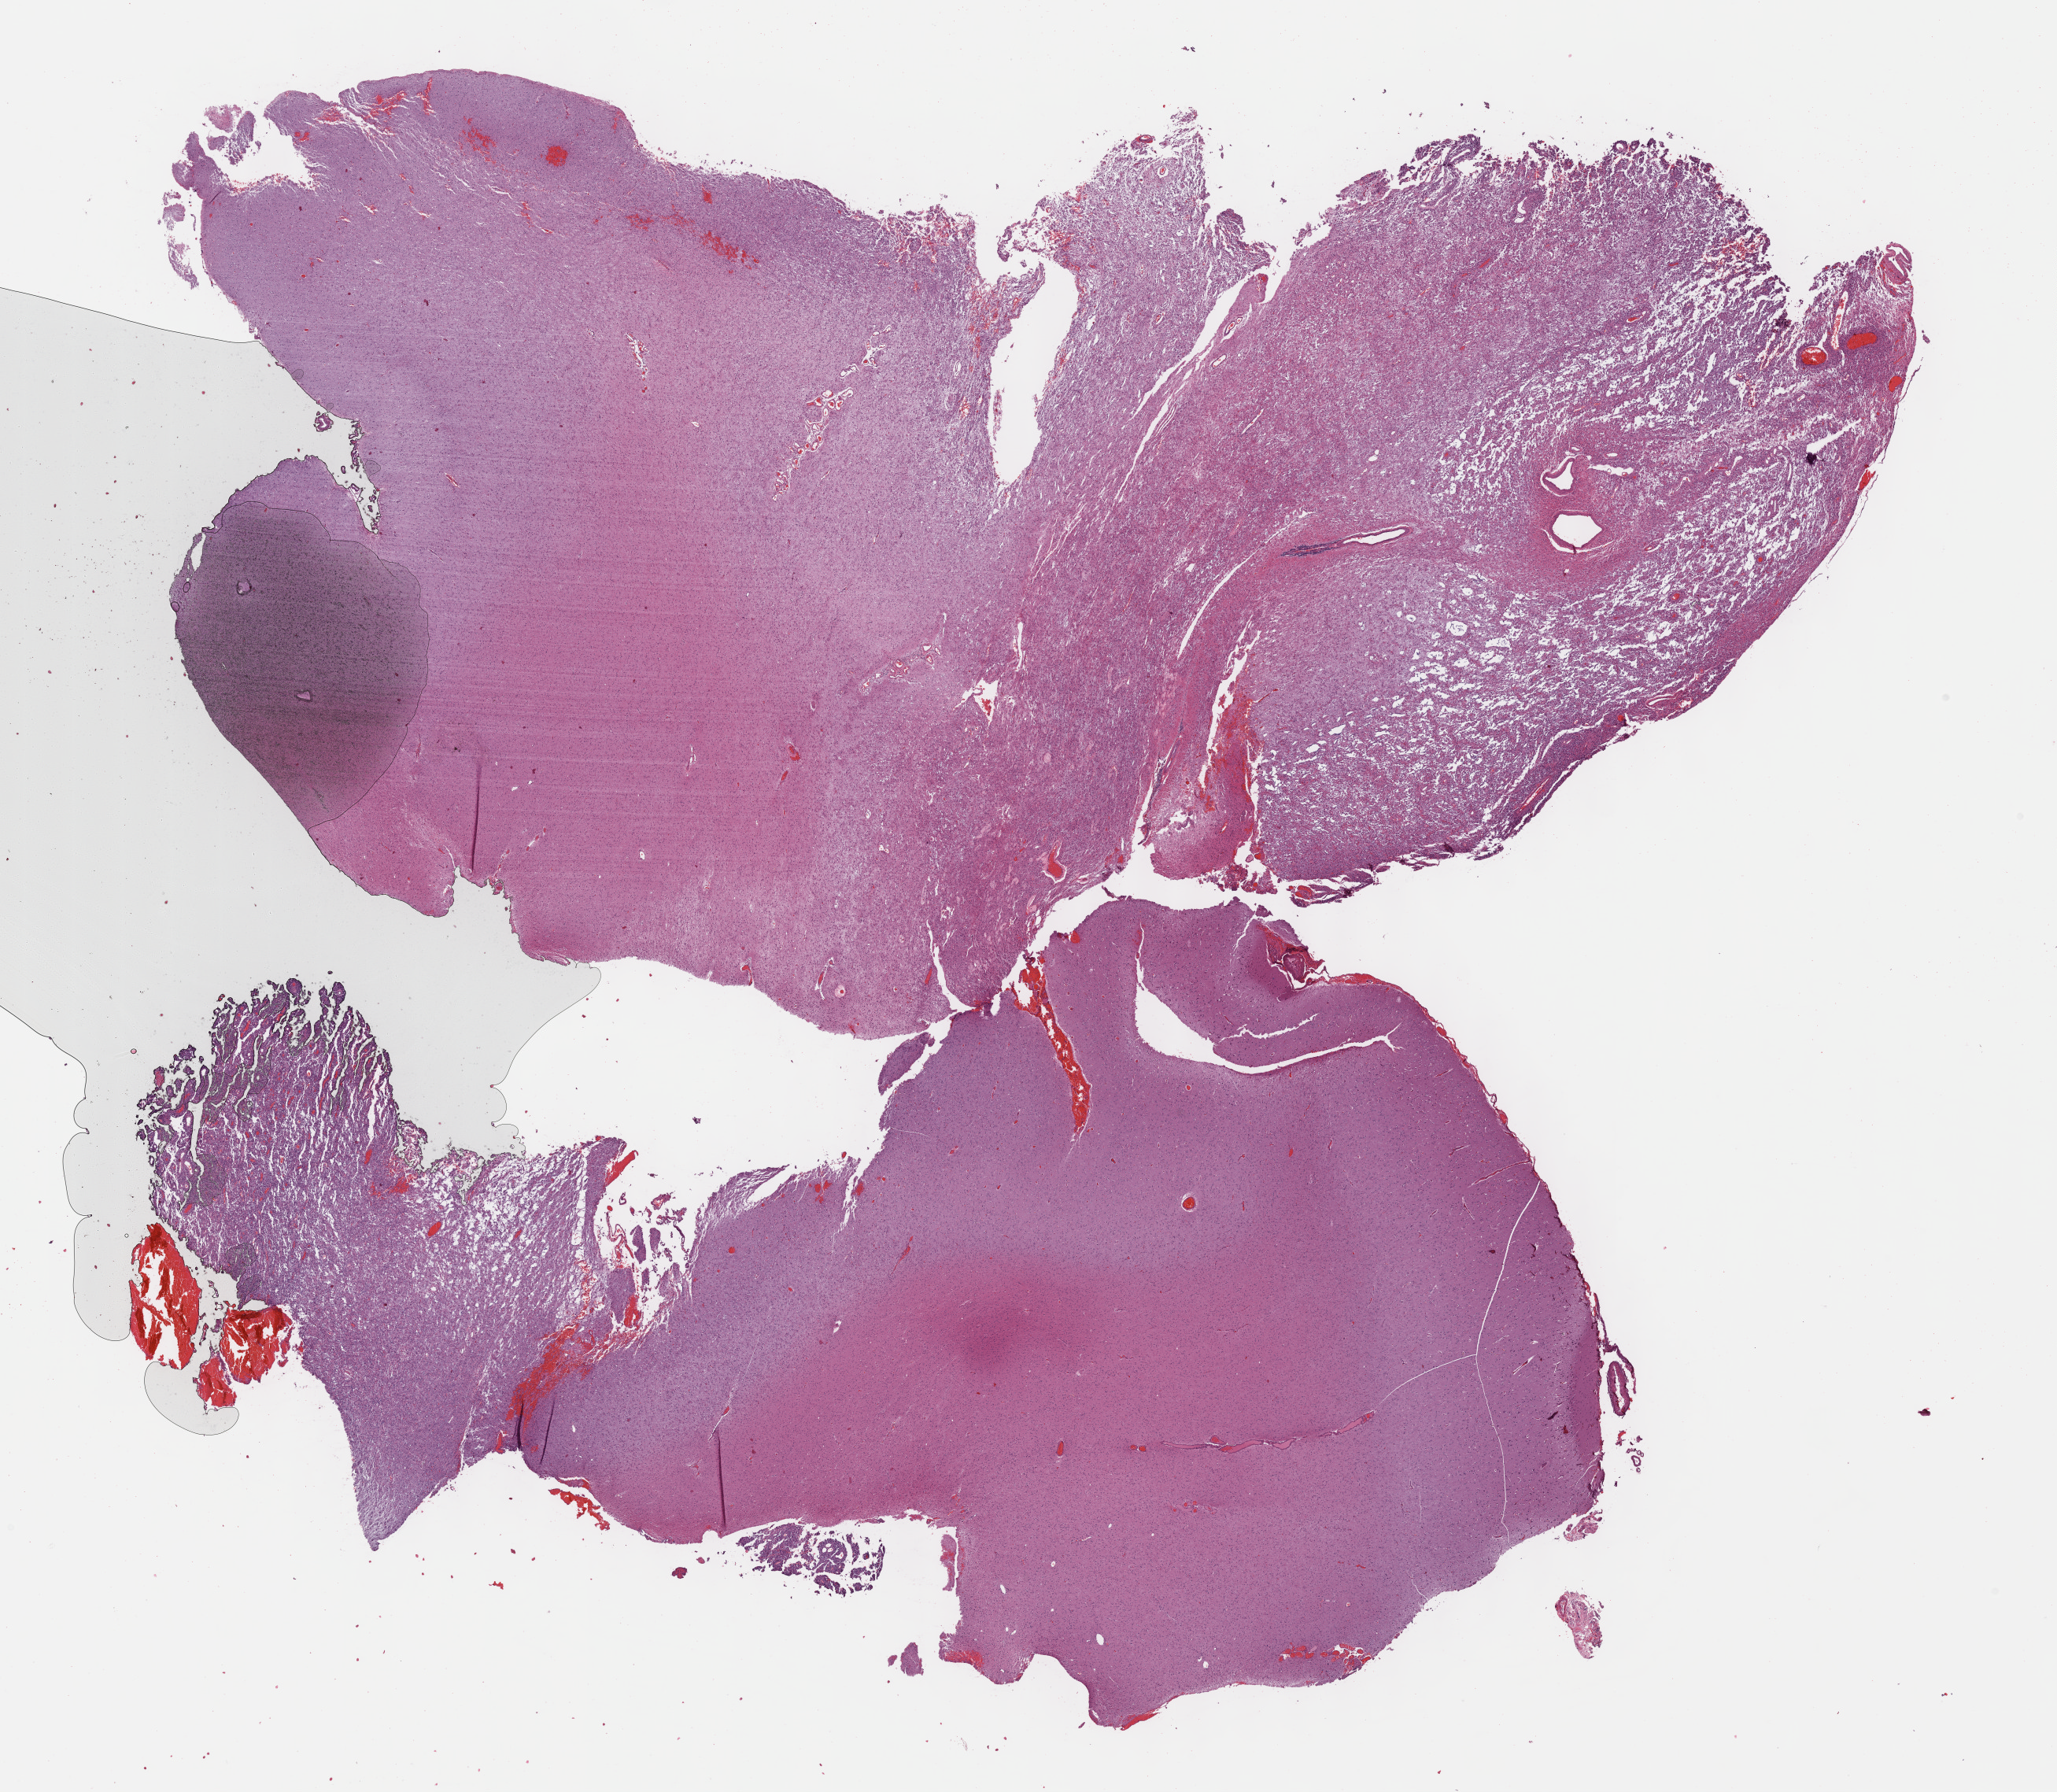
Digitized Hematoxylin and eosin (H&E) stained tissue section (whole slide) — whole scanned area (about 21.1 x 18.4 mm) shown as a low-resolution overview. FFPE section. Primary tumour sample from the brain. Male, age 58 years at initial diagnosis. Histologic grade: G3 (poorly differentiated).
Laterality: left. Histologic diagnosis: Mixed glioma.